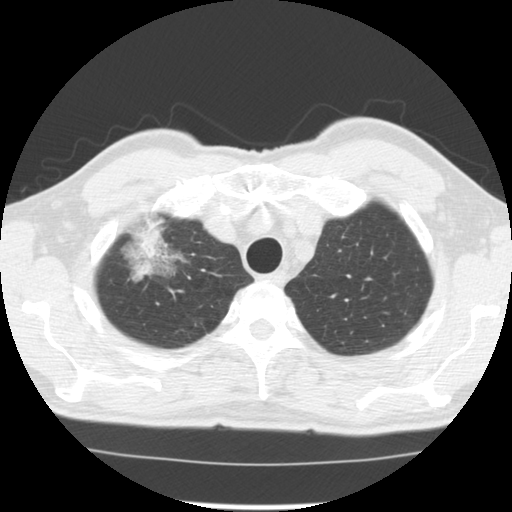
Chest CT (low-dose screening protocol), one axial image; third annual screen; lung window (W 1500 / L -600 HU); standard (soft-tissue) reconstruction kernel (STANDARD); slice 22 of 128 in the series. Male, age 64 years at enrolment. Former smoker at enrolment.
- Expert reader's lesion annotation, bounding box (x1, y1, x2, y2) in pixels: (122, 230, 194, 290).
- The screening reader recorded 3 non-calcified nodules or masses ≥4 mm on this exam; which of them this box marks is not recorded.
- Lung cancer was diagnosed 30 days after this screen: adenocarcinoma, NOS, right upper lobe, well differentiated (G1), stage IB (AJCC 6th edition), 45 mm at pathology.